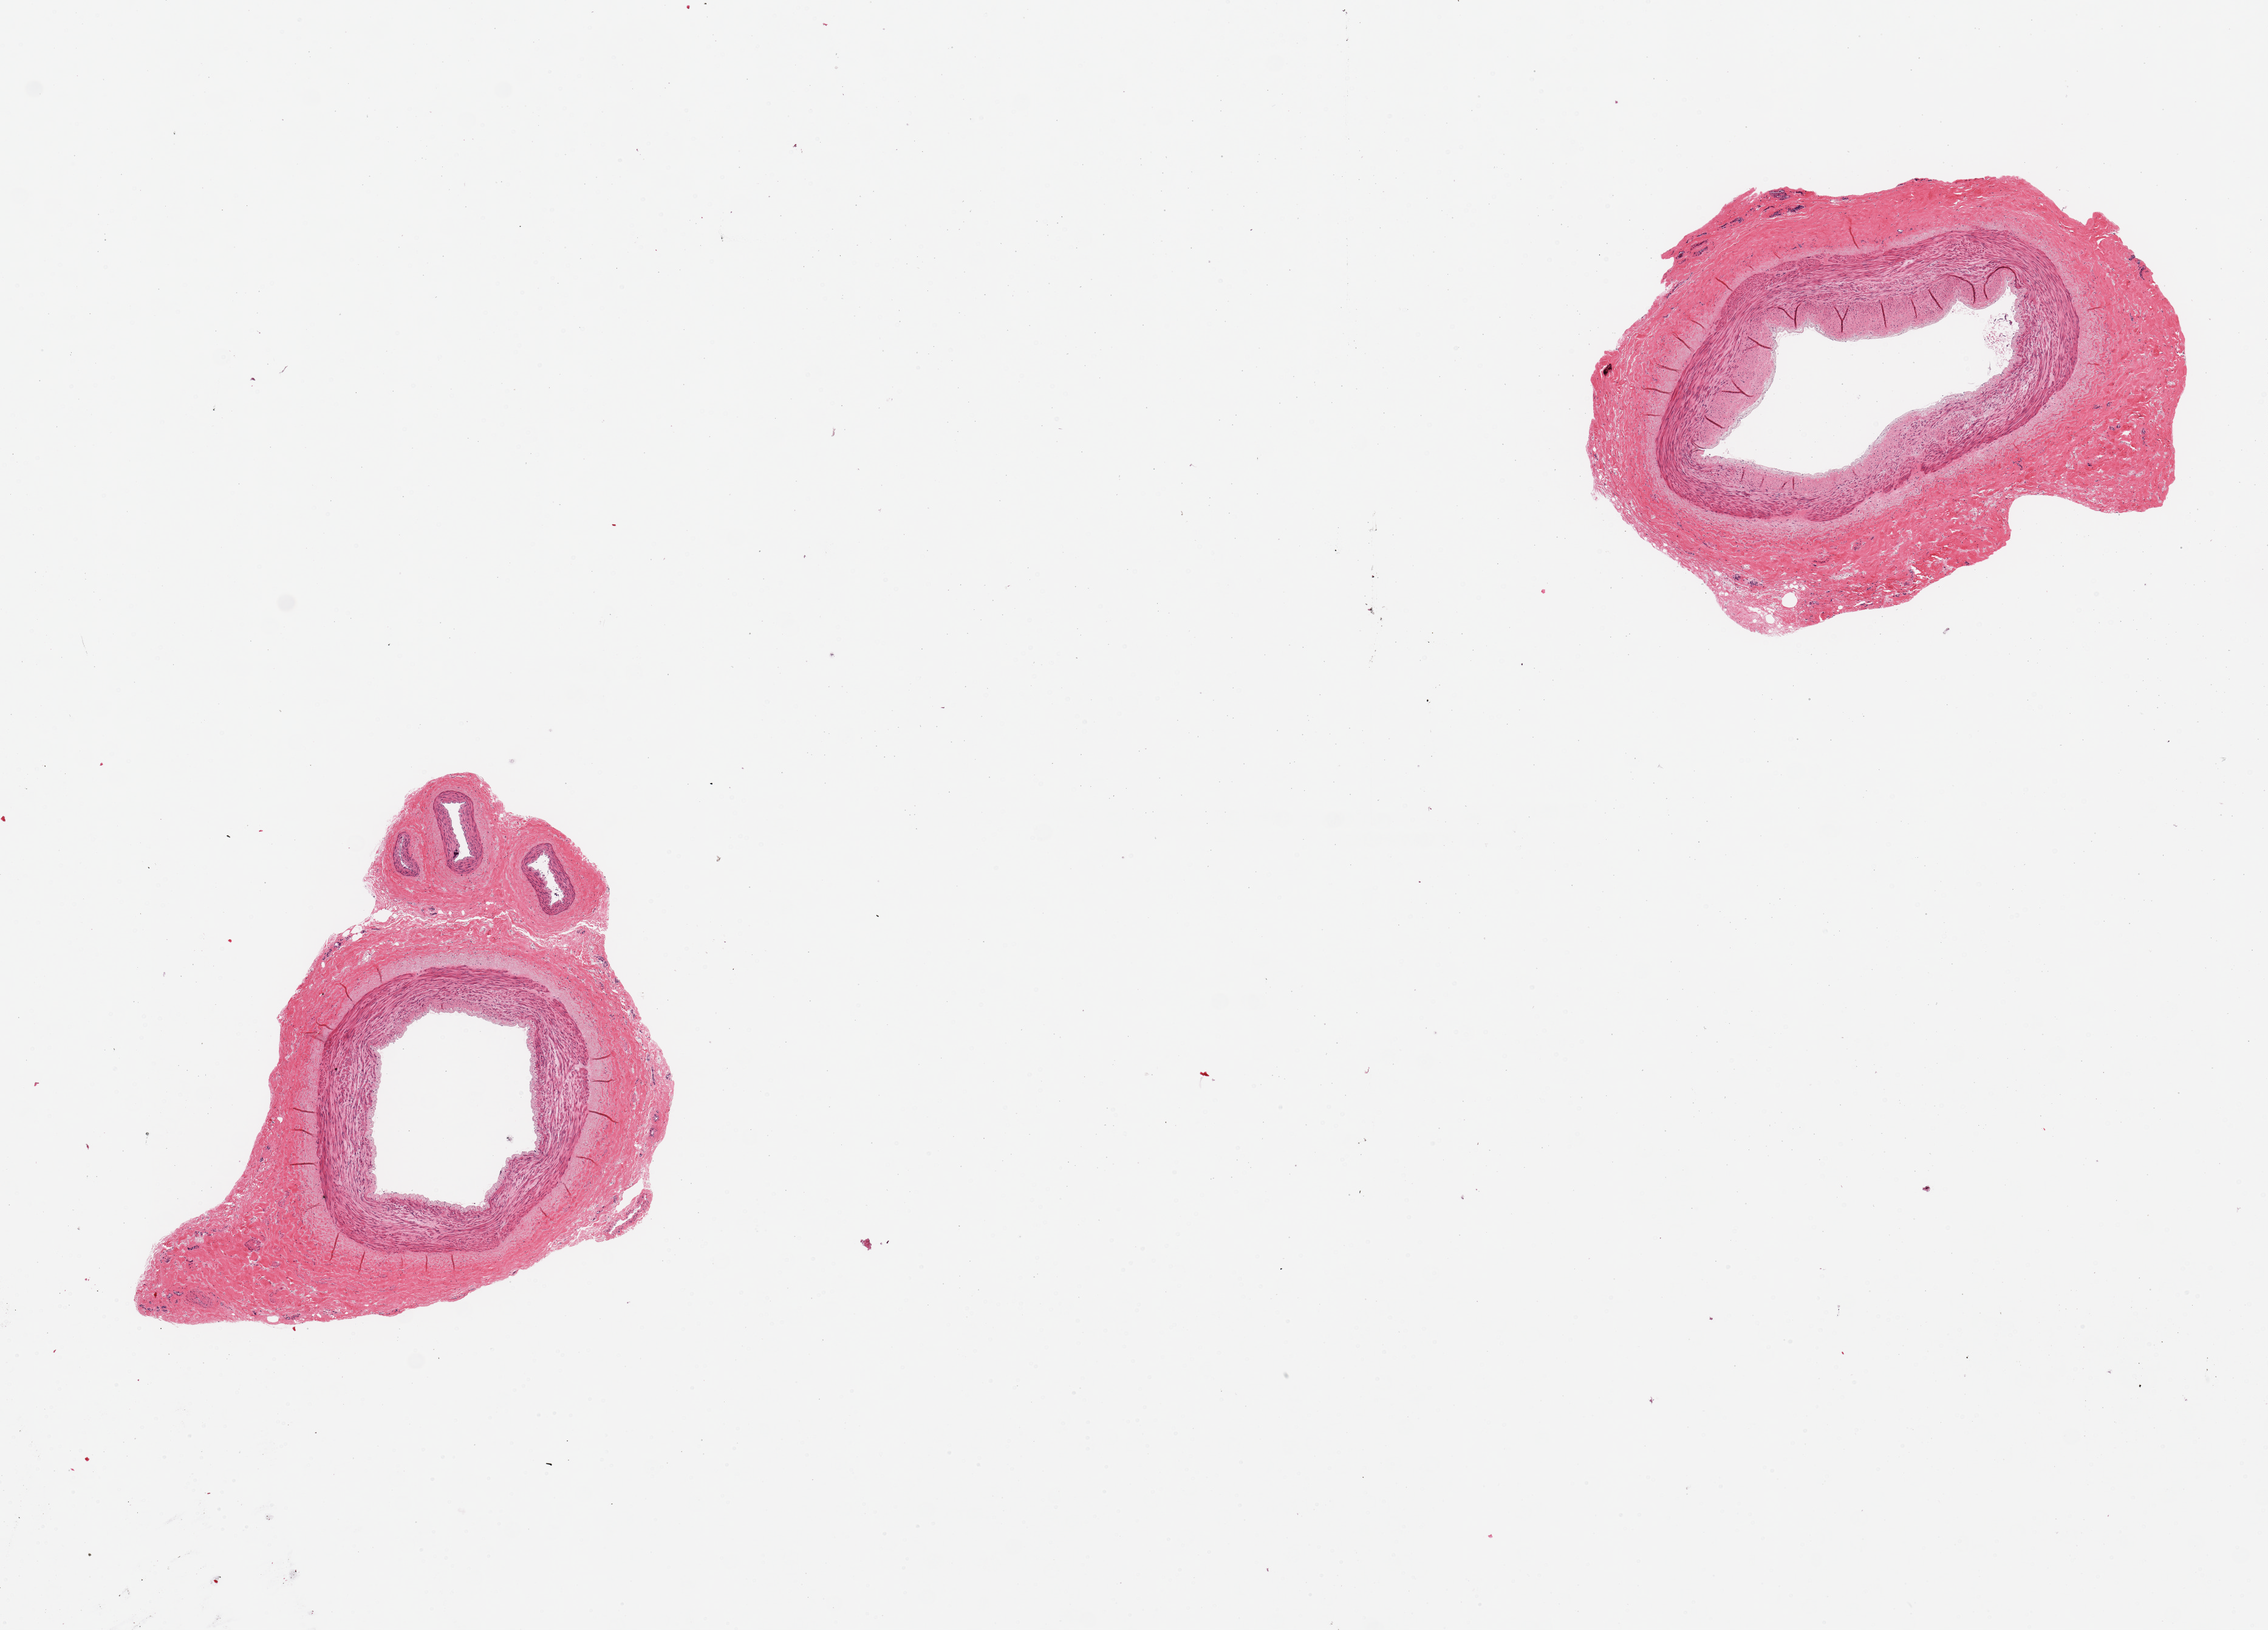
Whole-slide image, haematoxylin and eosin stain — shown as a low-resolution overview of the whole scanned area (about 14.8 x 10.6 mm, acquisition: 20x scan). PAXgene-fixed, paraffin-embedded tissue. Target tissue: tibial artery. Tissue donor sample. Donor sex: female.
Reviewer comment on this tissue sample: 2 pieces.